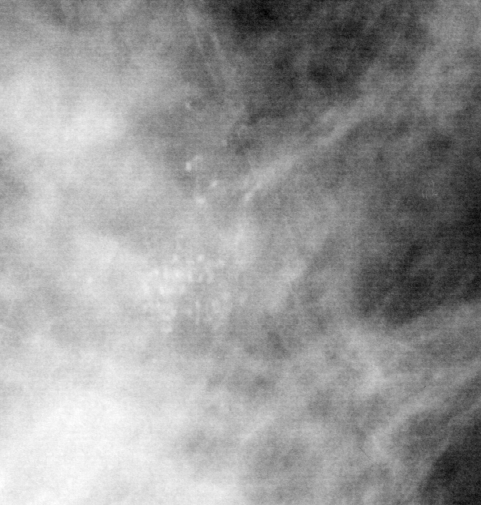
Region of interest cut from a scanned film mammogram (one marked finding), right breast, MLO view.
Marked abnormality: calcifications, morphology pleomorphic, distribution clustered; BI-RADS assessment category 5; subtlety rating 4 on a 1 (subtle) to 5 (obvious) scale; pathology (as recorded): malignant.